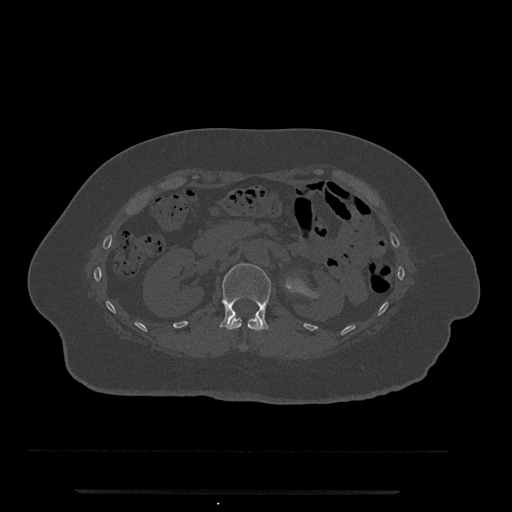
CT including the spine, one axial slice. Position 126 of 797 along the scan axis. Reconstruction kernel Br40s/3. 120 kVp. Bone window (W 1800 / L 400 HU). 0.5 mm slice thickness. 512 × 512 image matrix, field of view 440 × 440 mm. Female patient, age 51 years. From the clinical record (not read from this slice): primary cancer: neuro.
Annotated regions visible in this slice (semi-automatically segmented with operator editing):
- L1 vertebra: bounding box [x1, y1, x2, y2] px = [220, 263, 271, 329]
- T12 vertebra: [227, 317, 263, 350]